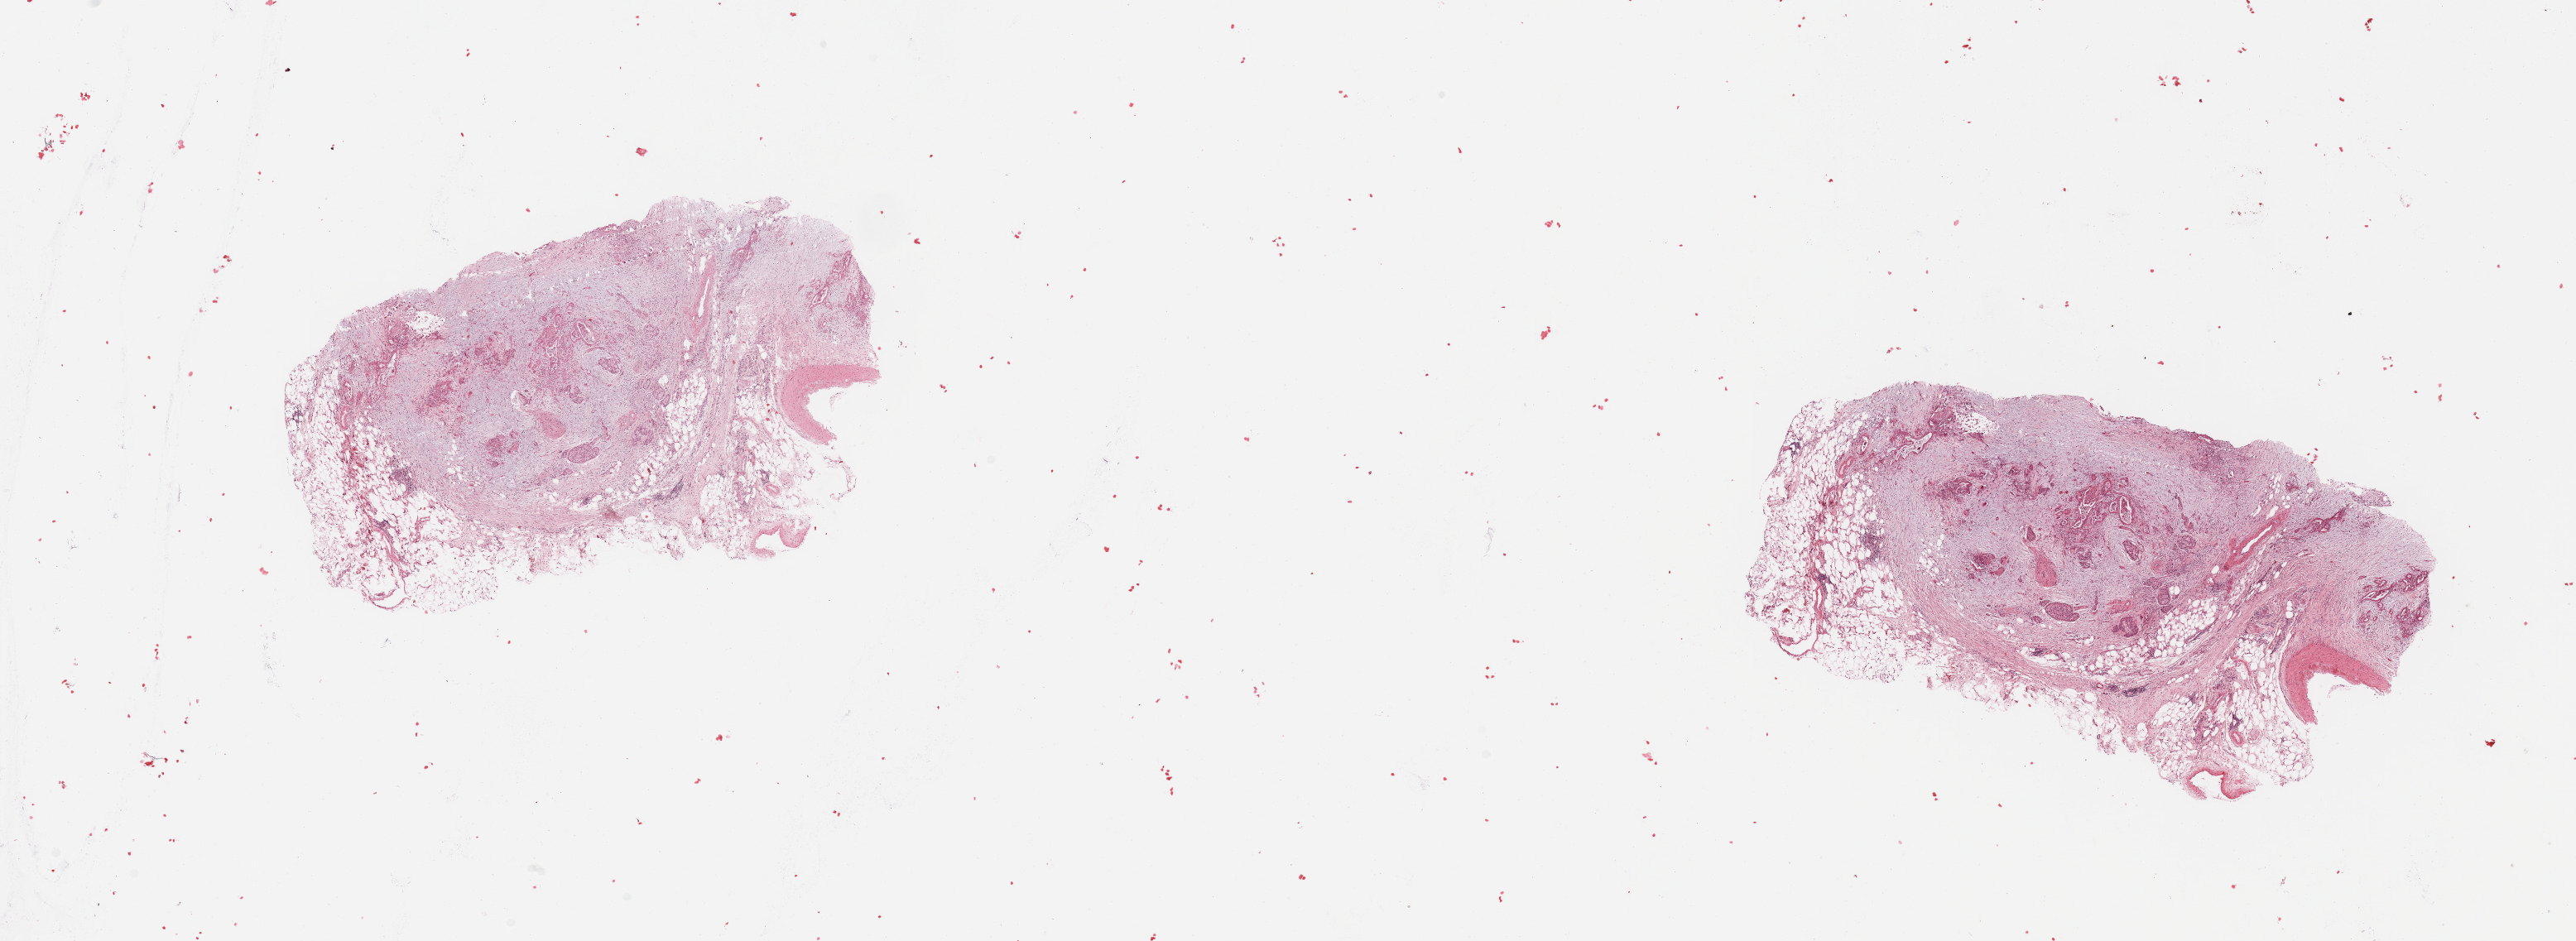
H&E whole-slide image — whole scanned area (about 24.6 x 9.0 mm, slide scanned at 20x) shown as a low-resolution overview; tumour tissue sample, sampled site: pancreas. 69-year-old female patient. Histologic grade: G3 (poorly differentiated). Pathologist review of this section (percent, as recorded): tumour nuclei 30%, necrosis 2%.
* diagnosis: Infiltrating duct carcinoma, NOS
* primary tumour site (as recorded): head
* AJCC pathologic stage: IIA